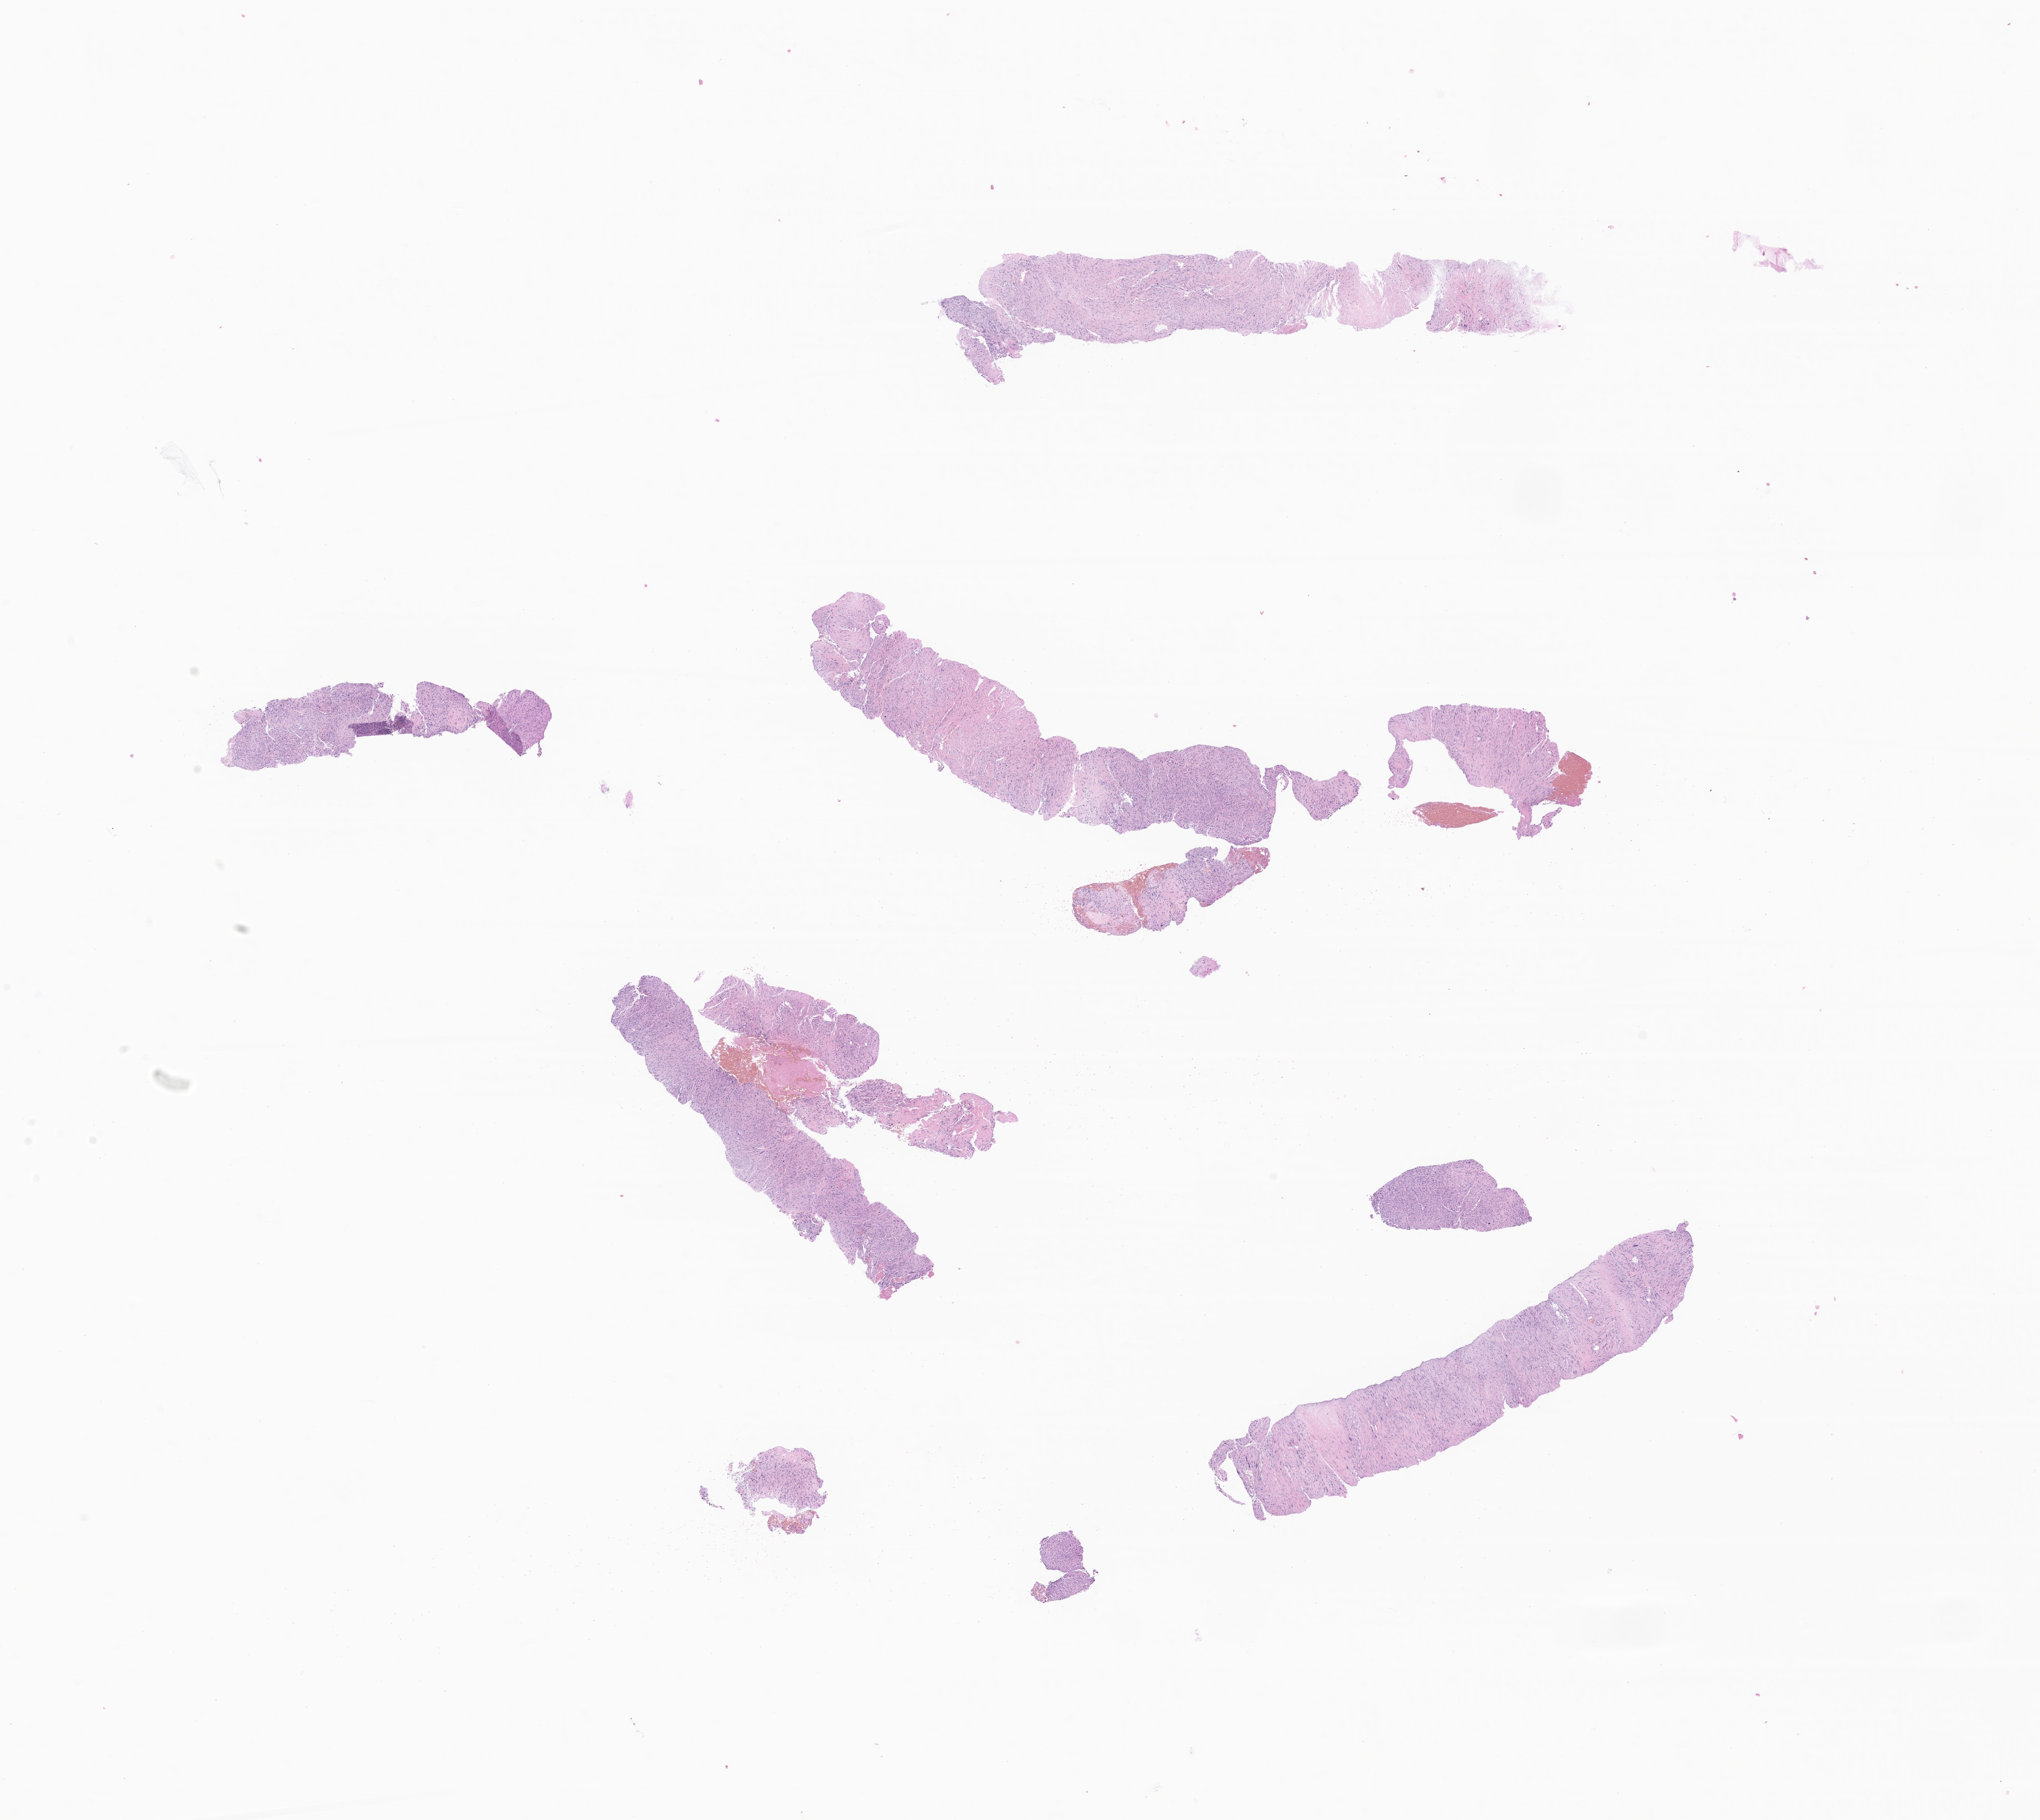
Digitized hematoxylin and eosin (H&E)-stained section of tumor tissue from the soft tissue of trunk — a low-resolution overview of the entire scanned area, about 17.9 x 16.0 mm, formalin-fixed paraffin-embedded section. Patient male; age 237 months (19 years 9 months).
Diagnosis (ICD-O-3 morphology term): Leiomyosarcoma, NOS.